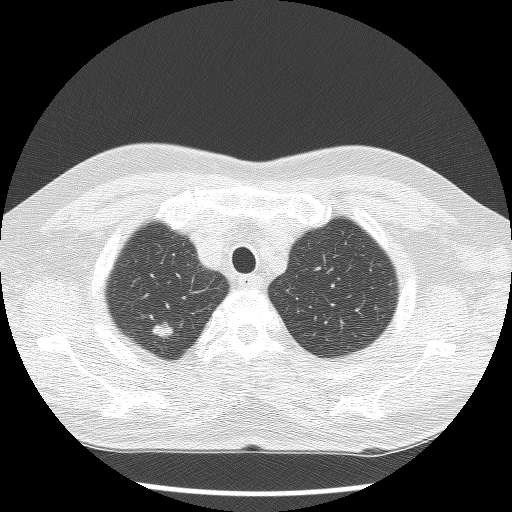
Low-dose screening chest CT, axial slice, baseline screening round, lung window (W 1500 / L -600 HU), slice 18 of 120 in the series, 512 × 512 image matrix. Male participant, aged 70 years at enrolment. Current smoker at enrolment.
Expert reader's lesion annotation, bounding box <137,314,184,353> (left, top, right, bottom; pixels). Screening reader's record for this exam (one nodule recorded; not confirmed to be the boxed lesion): non-calcified nodule or mass ≥4 mm, right upper lobe, 12 × 10 mm, smooth margins, soft tissue attenuation. Official screen result: positive, change unspecified: nodule(s) >= 4 mm or enlarging nodule(s), mass(es), or other non-specific abnormalities suspicious for lung cancer. Participant outcome: lung cancer diagnosed 14 days after this screen — large cell neuroendocrine carcinoma, right upper lobe, poorly differentiated (G3), stage IA (AJCC 6th edition), 15 mm at pathology.